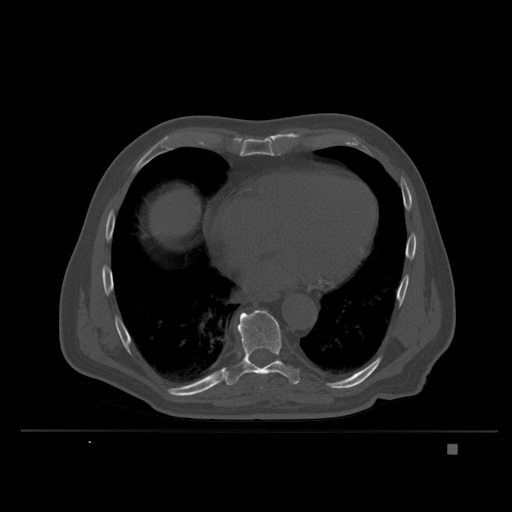
CT including the spine, one axial slice. Position 214 of 435 along the scan axis. Bone window (W 1800 / L 400 HU). 512 × 512 image matrix. Male patient, age 73 years. Case-level facts recorded for this patient, not image findings: primary cancer: skin.
Outlined on this slice (semi-automatically segmented with operator editing):
- T9 vertebra: bounding box [x1, y1, x2, y2] px = [224, 310, 300, 389]